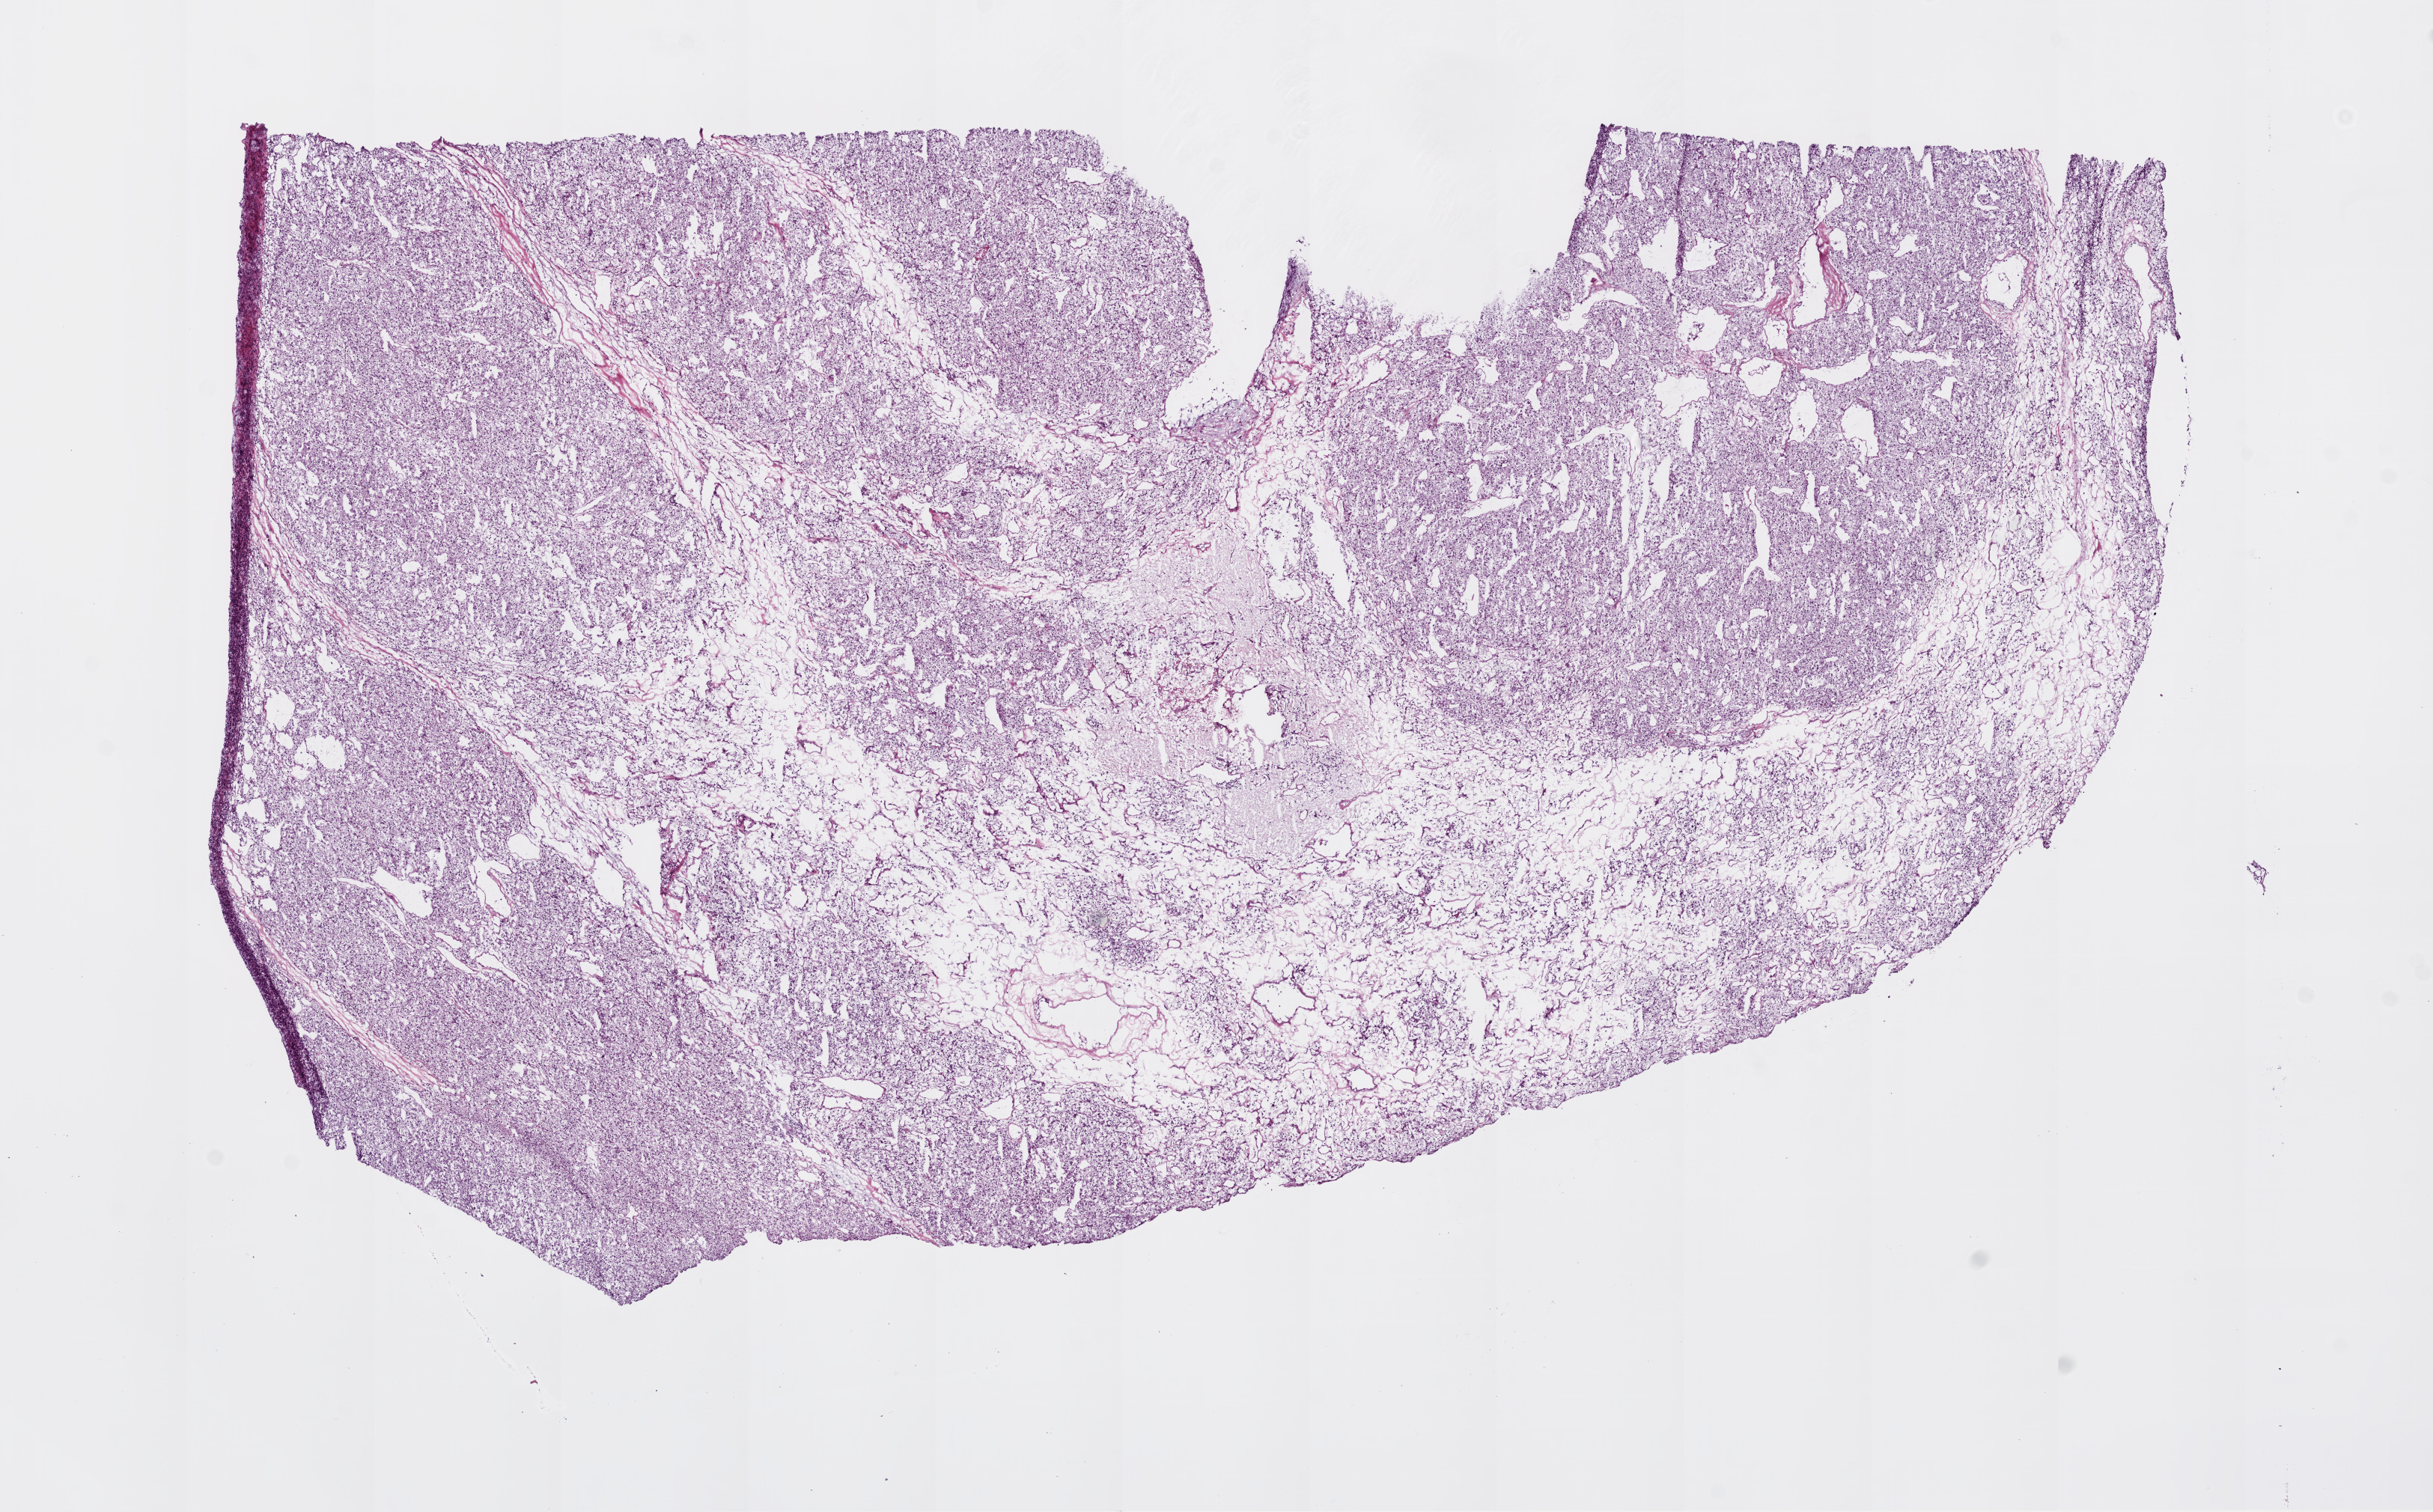
Whole-slide histology image, H&E-stained, low-resolution overview of the scanned area, about 13.0 x 8.1 mm (acquisition: 20x scan). Frozen section from the bottom of the tissue portion. Primary tumour sample from the kidney. Male patient; age at initial diagnosis 74 years. Histologic grade: G3 (poorly differentiated). Composition of this section per pathologist review: tumour cells 75%, tumour nuclei 85%, normal cells 0%, stromal cells 25%, necrosis 0%.
* lymph nodes positive (case pathology): 2 of 2 examined
* AJCC pathologic stage: III
* pathologic diagnosis: Clear cell adenocarcinoma, NOS